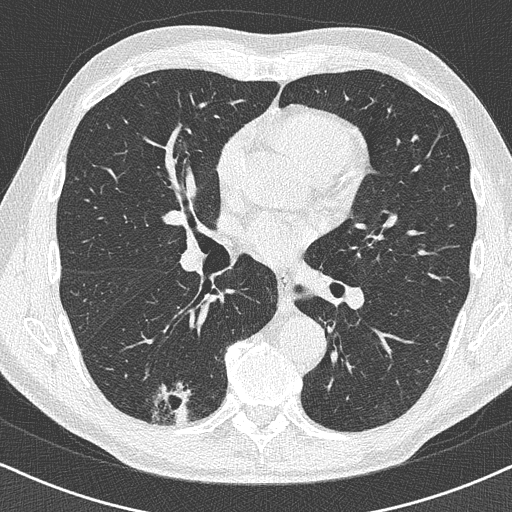
Low-dose screening chest CT, one axial slice; position 228 of 438 along the scan axis; reconstruction kernel B50f; lung window (W 1500 / L -600 HU); 1 mm slice thickness; 512 × 512 image matrix, field of view 320 × 320 mm.
Annotated regions visible in this slice (expert manual segmentation):
- lesion 1 (tumor, lower lobe of right lung): box from (x=175, y=404) to (x=189, y=425) px